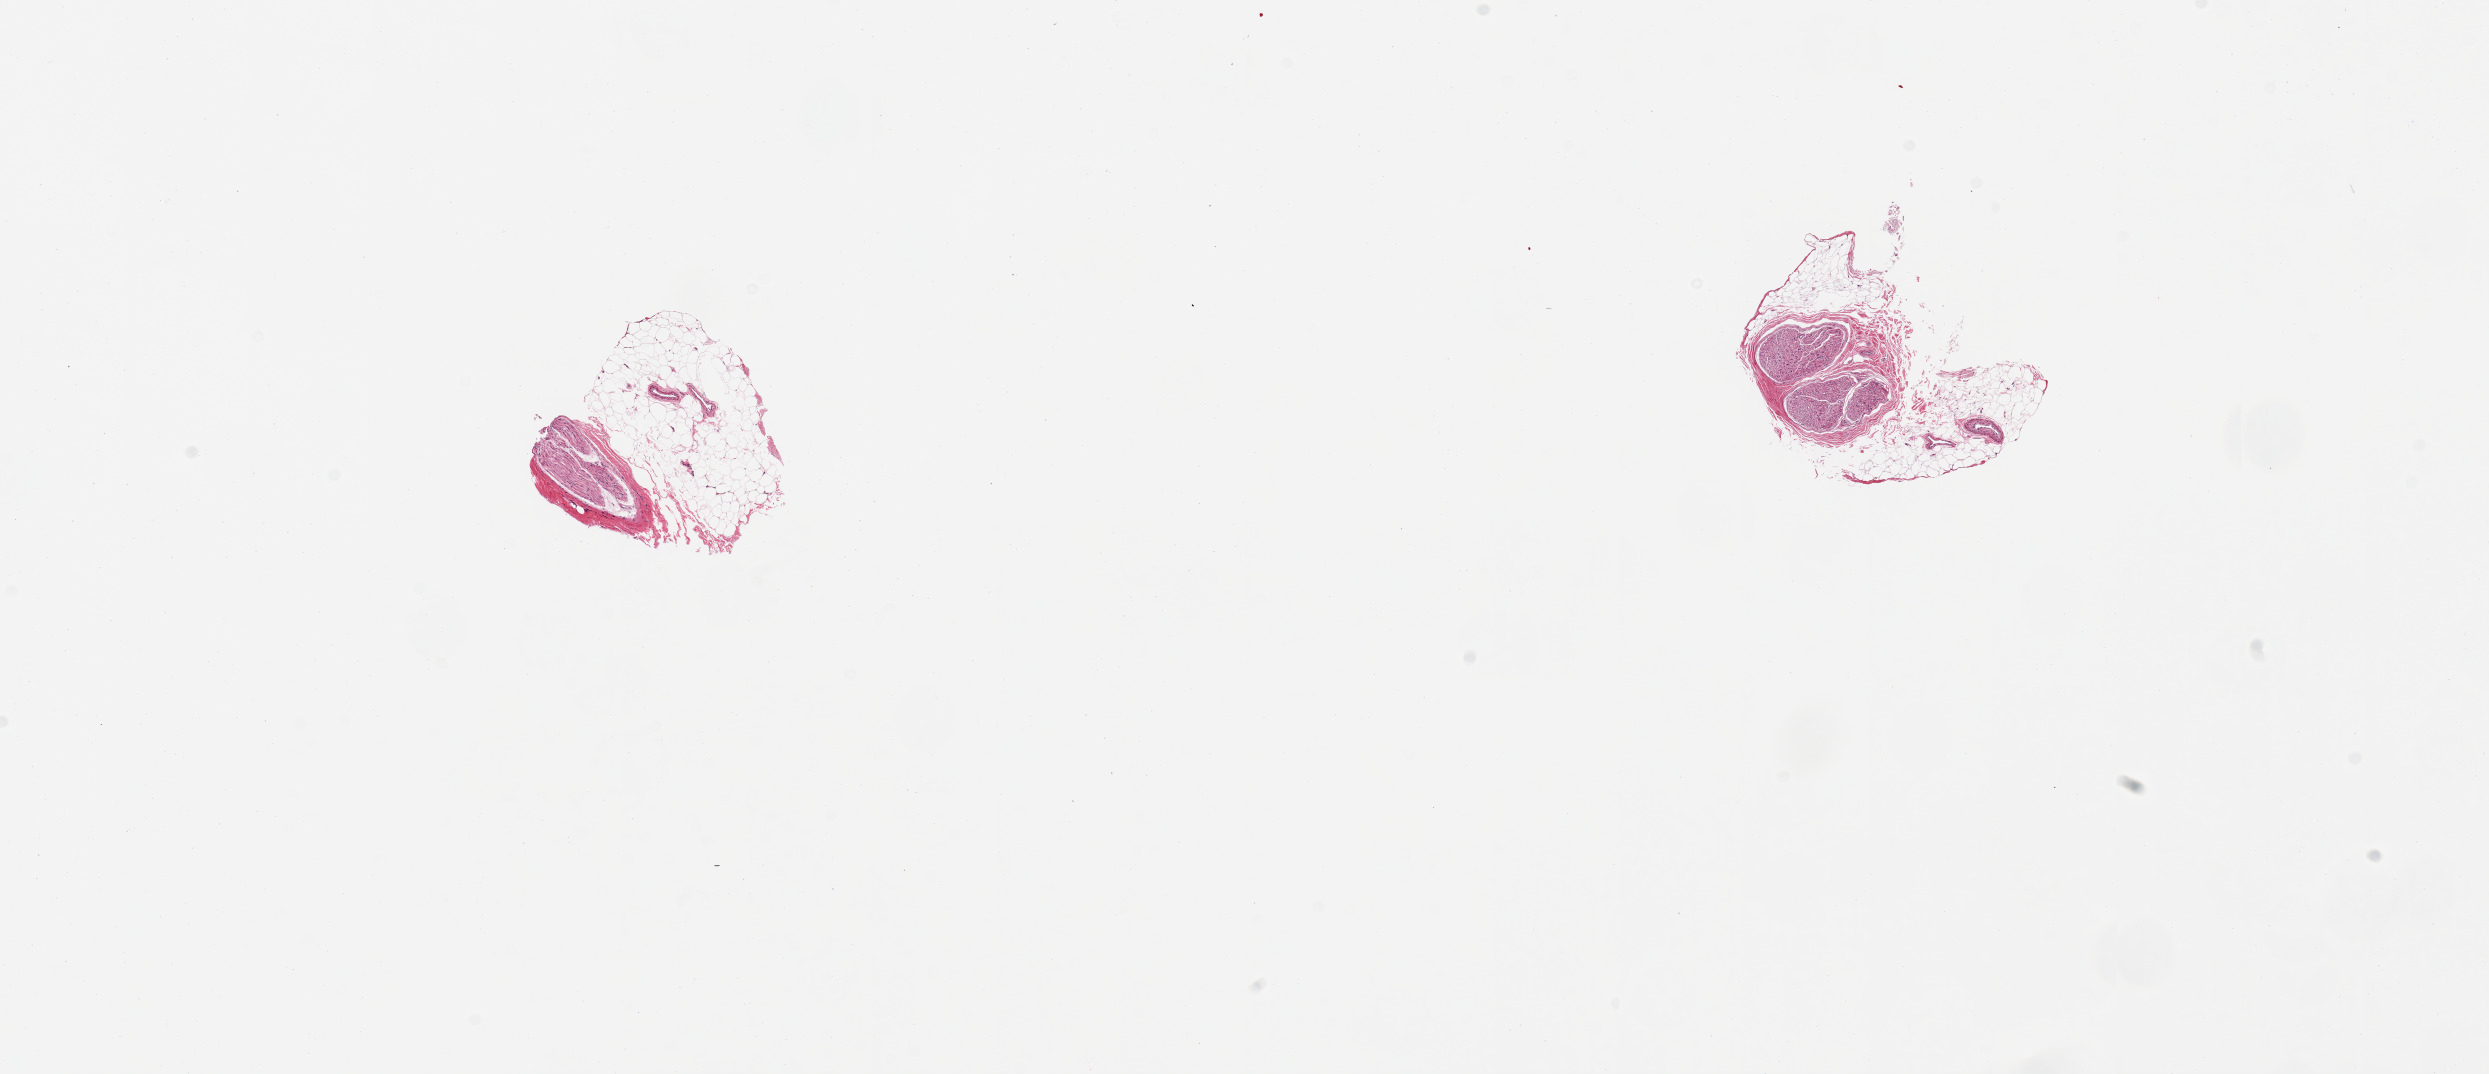
Hematoxylin and eosin (H&E) whole-slide image — whole scanned area (about 19.7 x 8.5 mm, slide scanned at 20x) shown as a low-resolution overview; PAXgene-fixed paraffin-embedded (PFPE) section; sampled site (target tissue): tibial nerve; donor tissue sample. Donor: female.
- review note (as recorded): 2 very small 1 mm nerves with excessive (60 & 50%) external fat